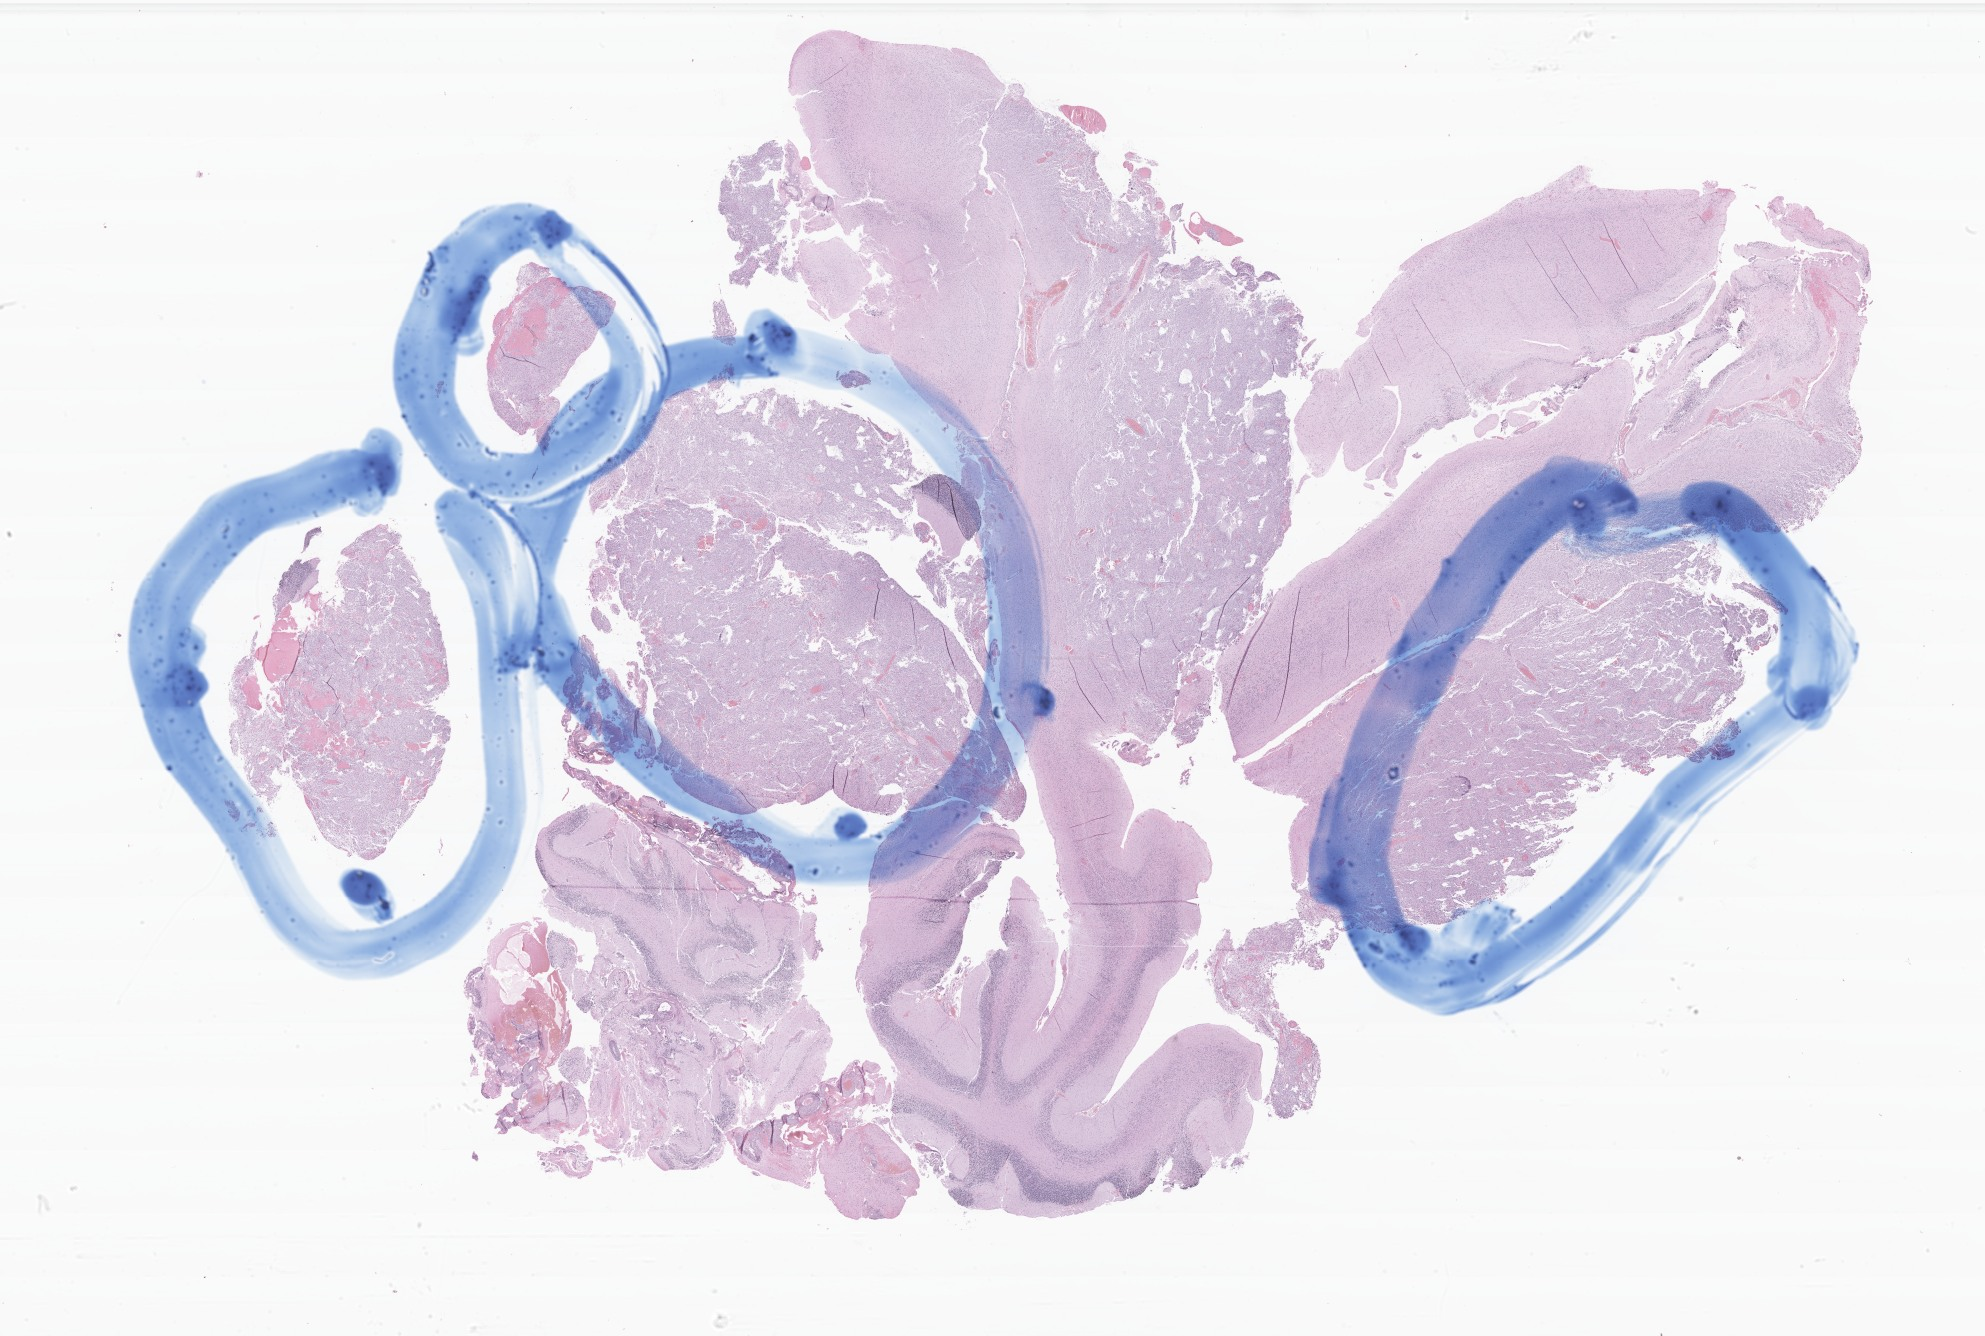
Hematoxylin and eosin (H&E) whole-slide image of tumor tissue from the cerebellum, whole scanned area (about 33.4 x 22.5 mm) shown as a low-resolution overview; formalin-fixed, paraffin-embedded (FFPE) tissue. Patient male; age 113 months (9 years 5 months).
* diagnosis (ICD-O-3 morphology term): Pilocytic astrocytoma